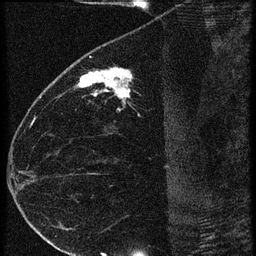
Breast MRI (dynamic contrast-enhanced), one sagittal slice; 3 images stored at this slice position (order not interpretable as contrast timing); 1.5 T; TE 4.2 ms, TR 20.4 ms; 256 × 256 image matrix, field of view 180 × 180 mm. Female patient, age 35 years. From the clinical record (not read from this slice): setting: breast cancer imaged before/during neoadjuvant chemotherapy; receptor status: HR-positive, HER2-negative.
Annotated regions visible in this slice (semi-automatic segmentation, software-assisted and operator-edited):
- analysis volume of interest (the breast-tissue region the enhancement analysis was run in; not a lesion): bounding box <65,60,169,119> (left, top, right, bottom; pixels)
- tumour enhancement mask (voxels above the 90 % enhancement threshold inside the analysis volume of interest): <78,68,132,101>